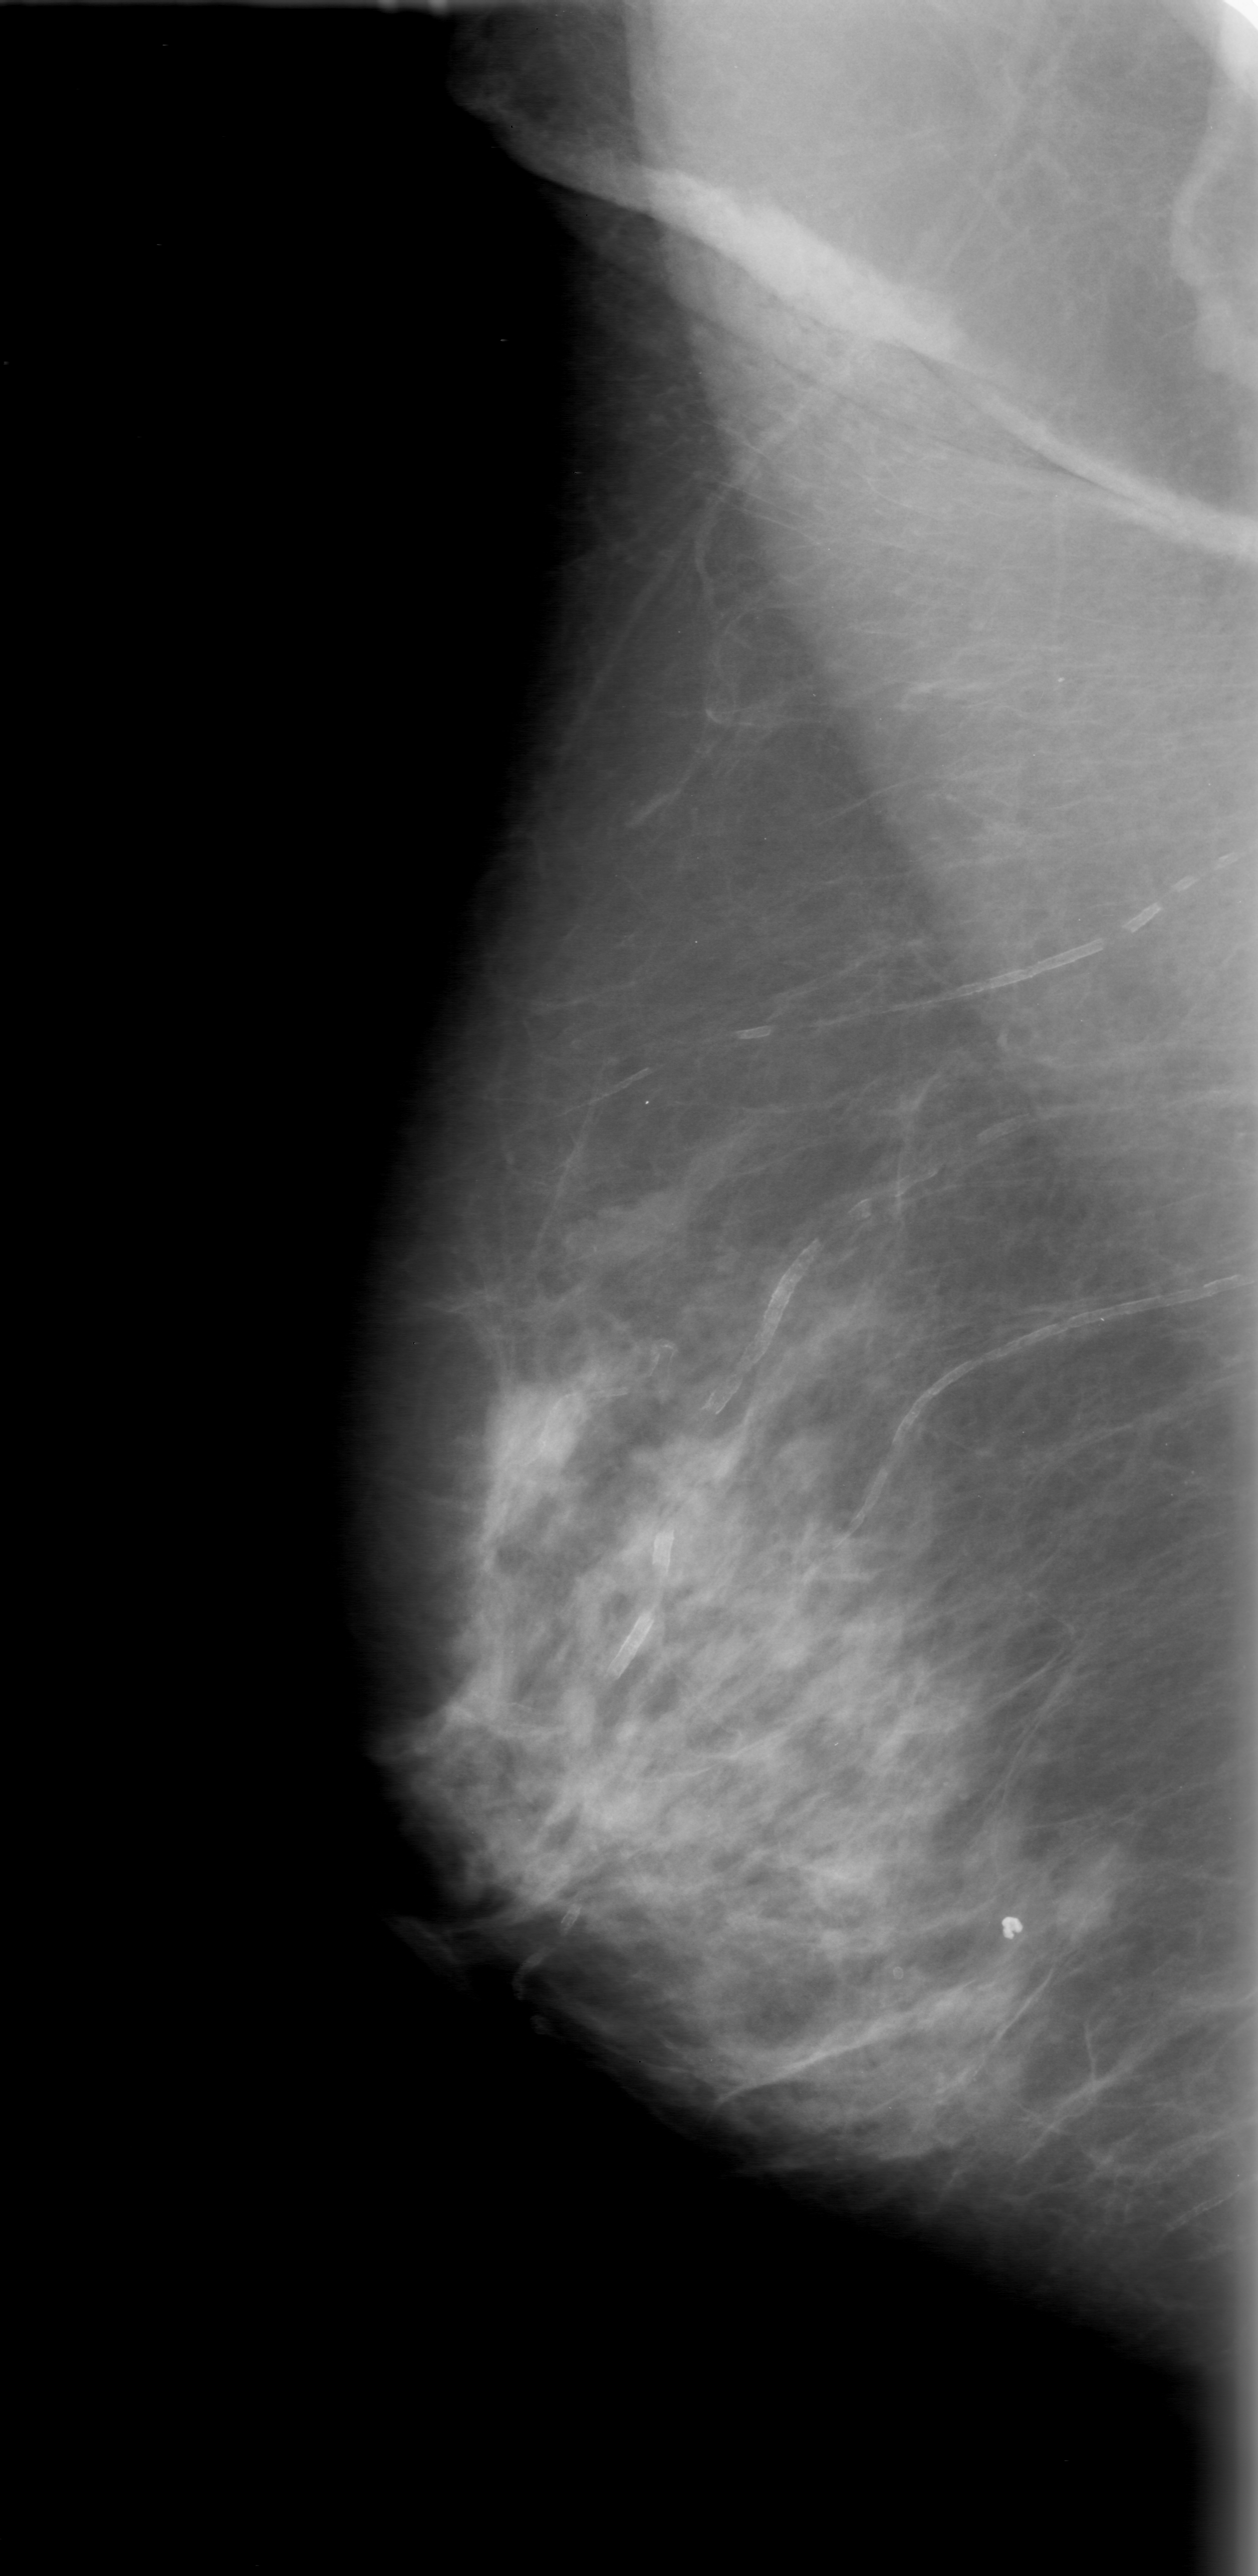
Mammogram (digitized film); right breast; MLO view; breast composition: scattered fibroglandular densities (BI-RADS density category 2 of 4).
Mass, shape round, margins obscured; BI-RADS assessment category 0; pathology result (as recorded, not read from the image): benign.